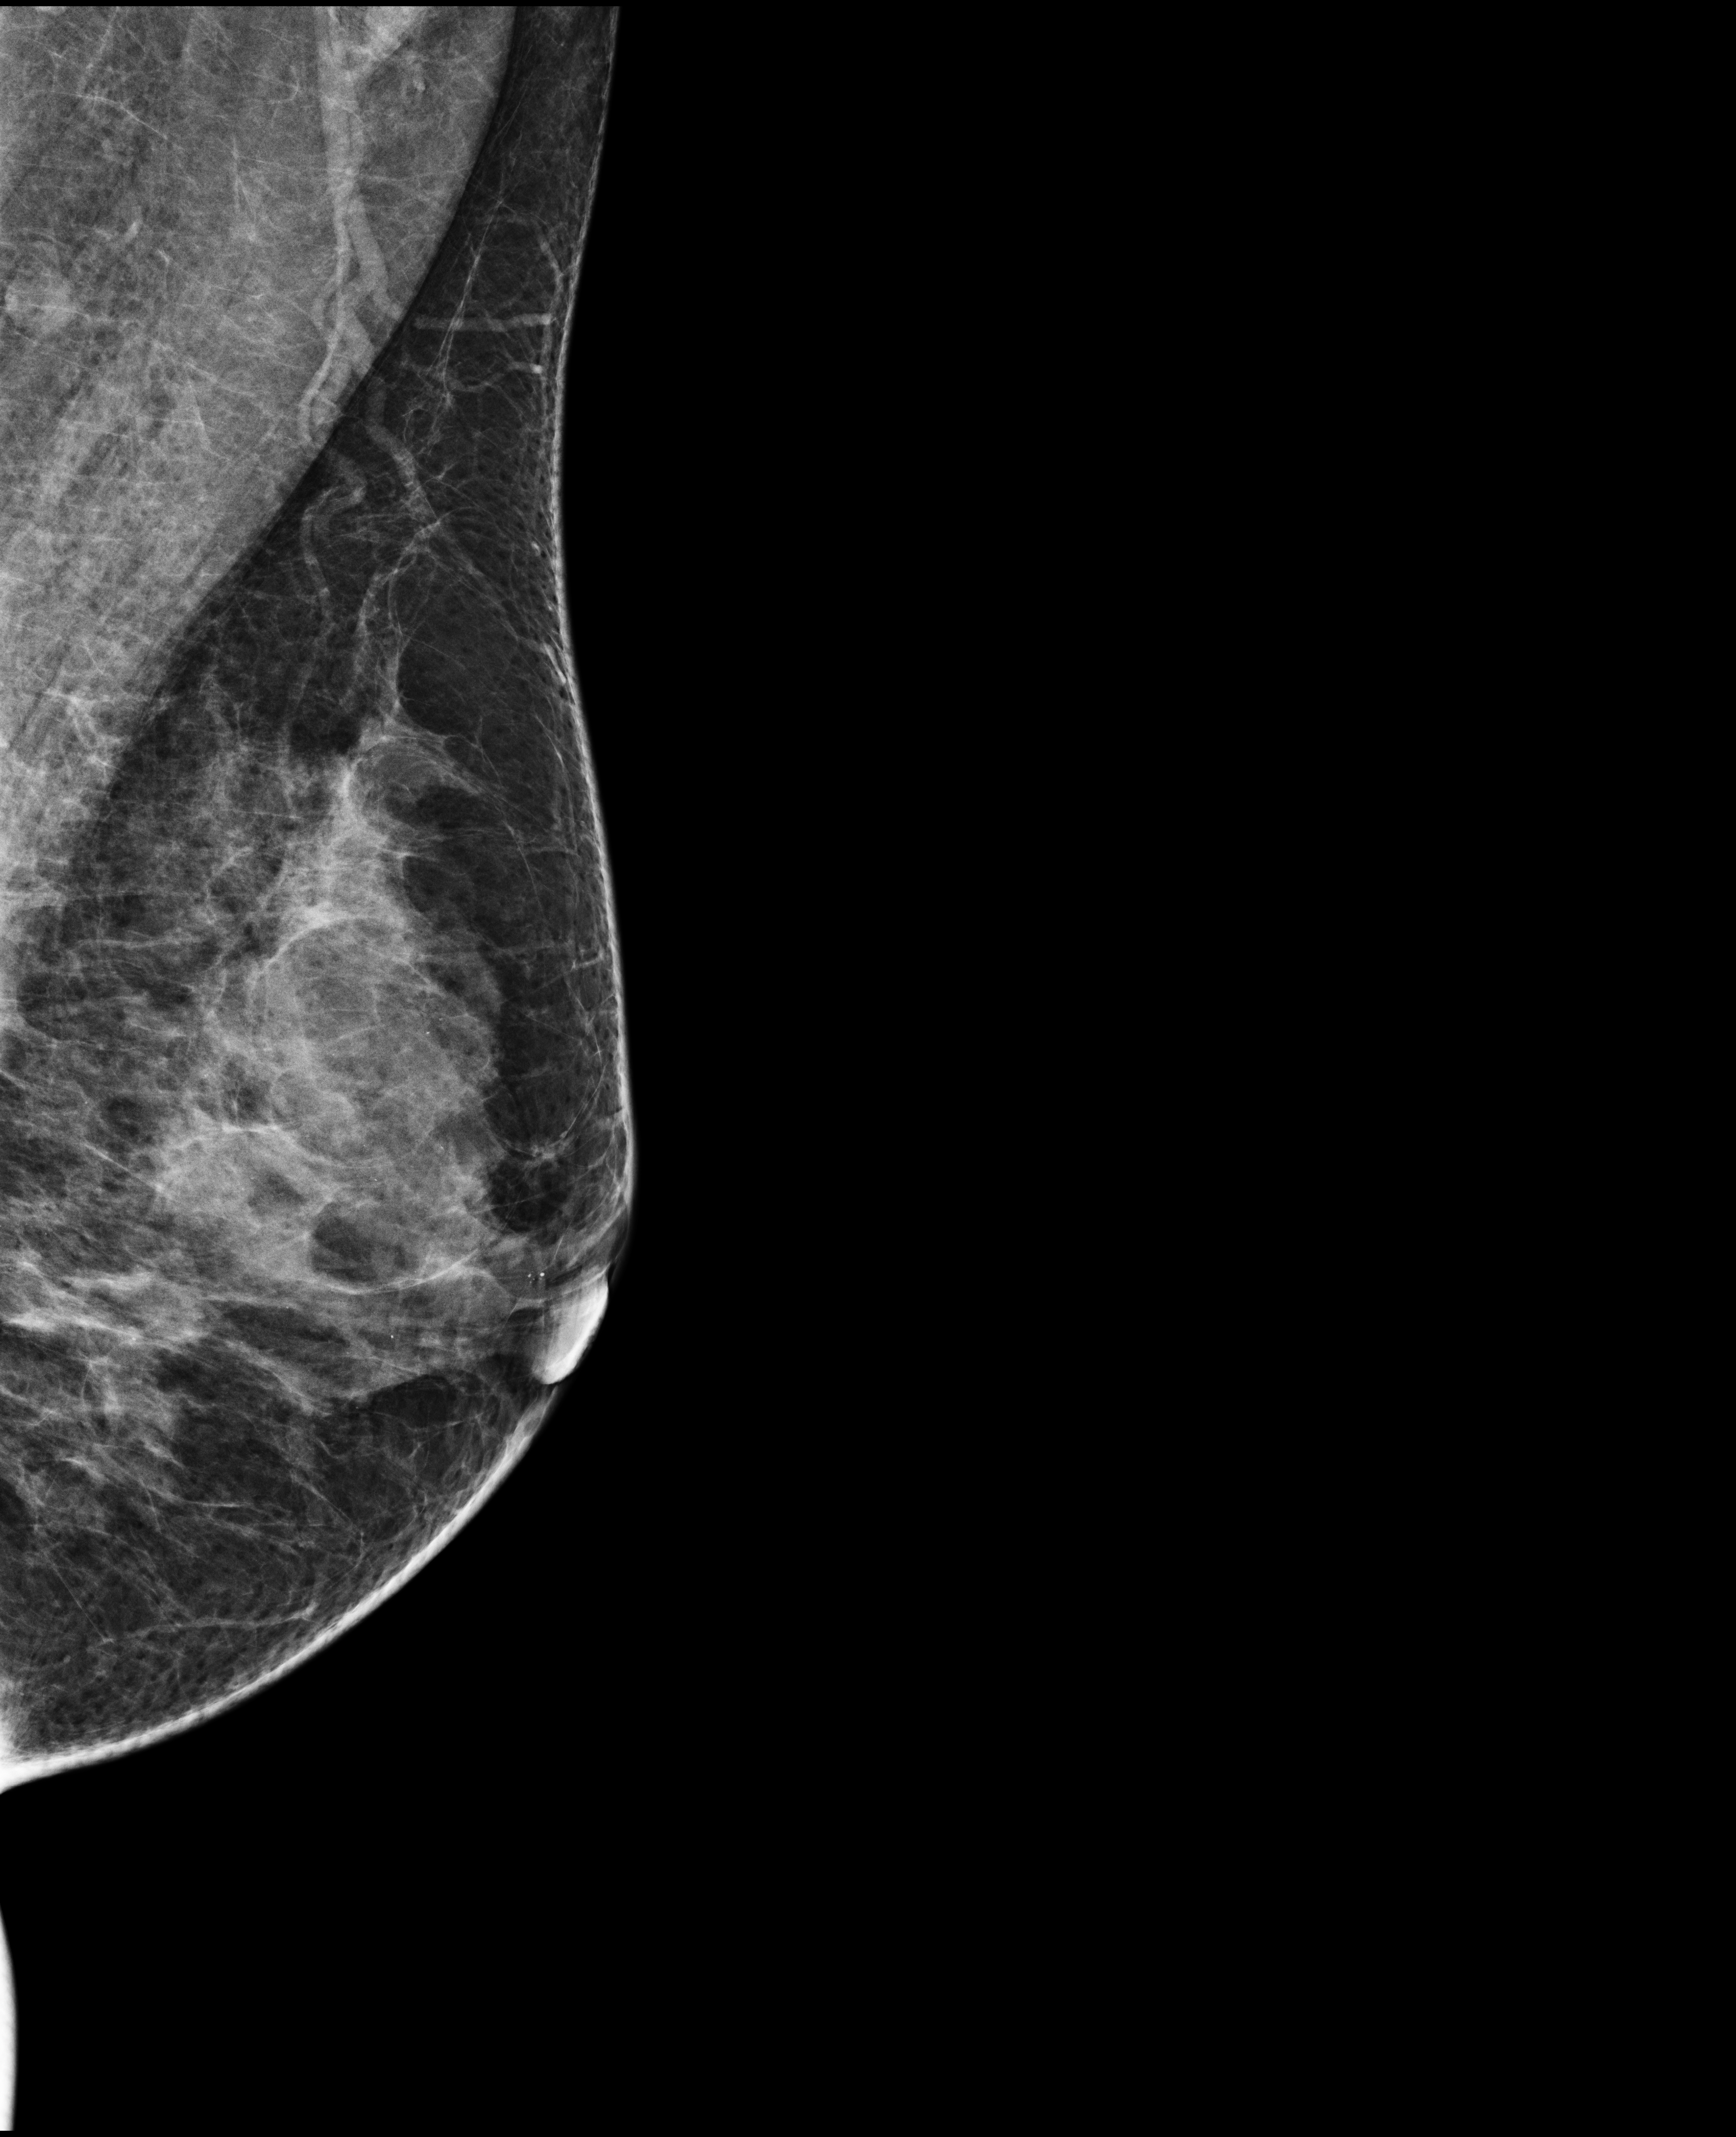
Full-field digital mammogram (FFDM), left breast, MLO view, annual screening mammography examination, compressed breast thickness 51 mm. Female patient, age 48 years.
- breast density at the screening exam (both breasts): heterogeneously dense (BI-RADS density category c)
- final BI-RADS category for the screening round (tomosynthesis exam, both breasts): category 4
- recall: recalled for additional imaging after this screen